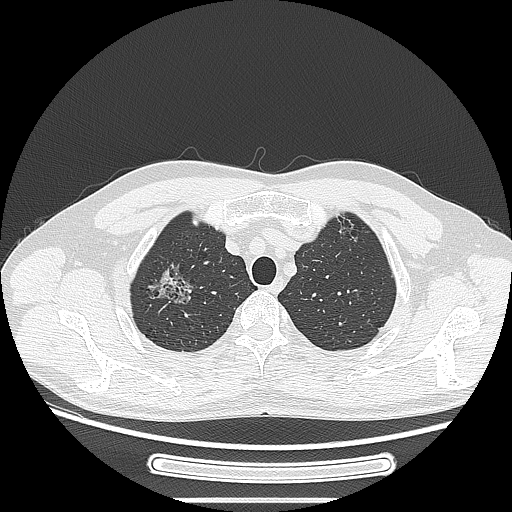
Chest CT, one axial slice. Slice 223 of 269 in the series (ordered by position). 120 kVp. Lung window (W 1500 / L -600 HU). 512 × 512 image matrix, field of view 382 × 382 mm. Male patient, age 53 years. Case-level facts recorded for this patient, not image findings: clinical TNM (as recorded): T1c N0 M0; histopathological grade: G2.
Structures marked on this image (rectangle marked by the reading radiologist):
- lung tumour (recorded histology: adenocarcinoma): bounding box (x1, y1, x2, y2) in pixels: (142, 256, 198, 308)